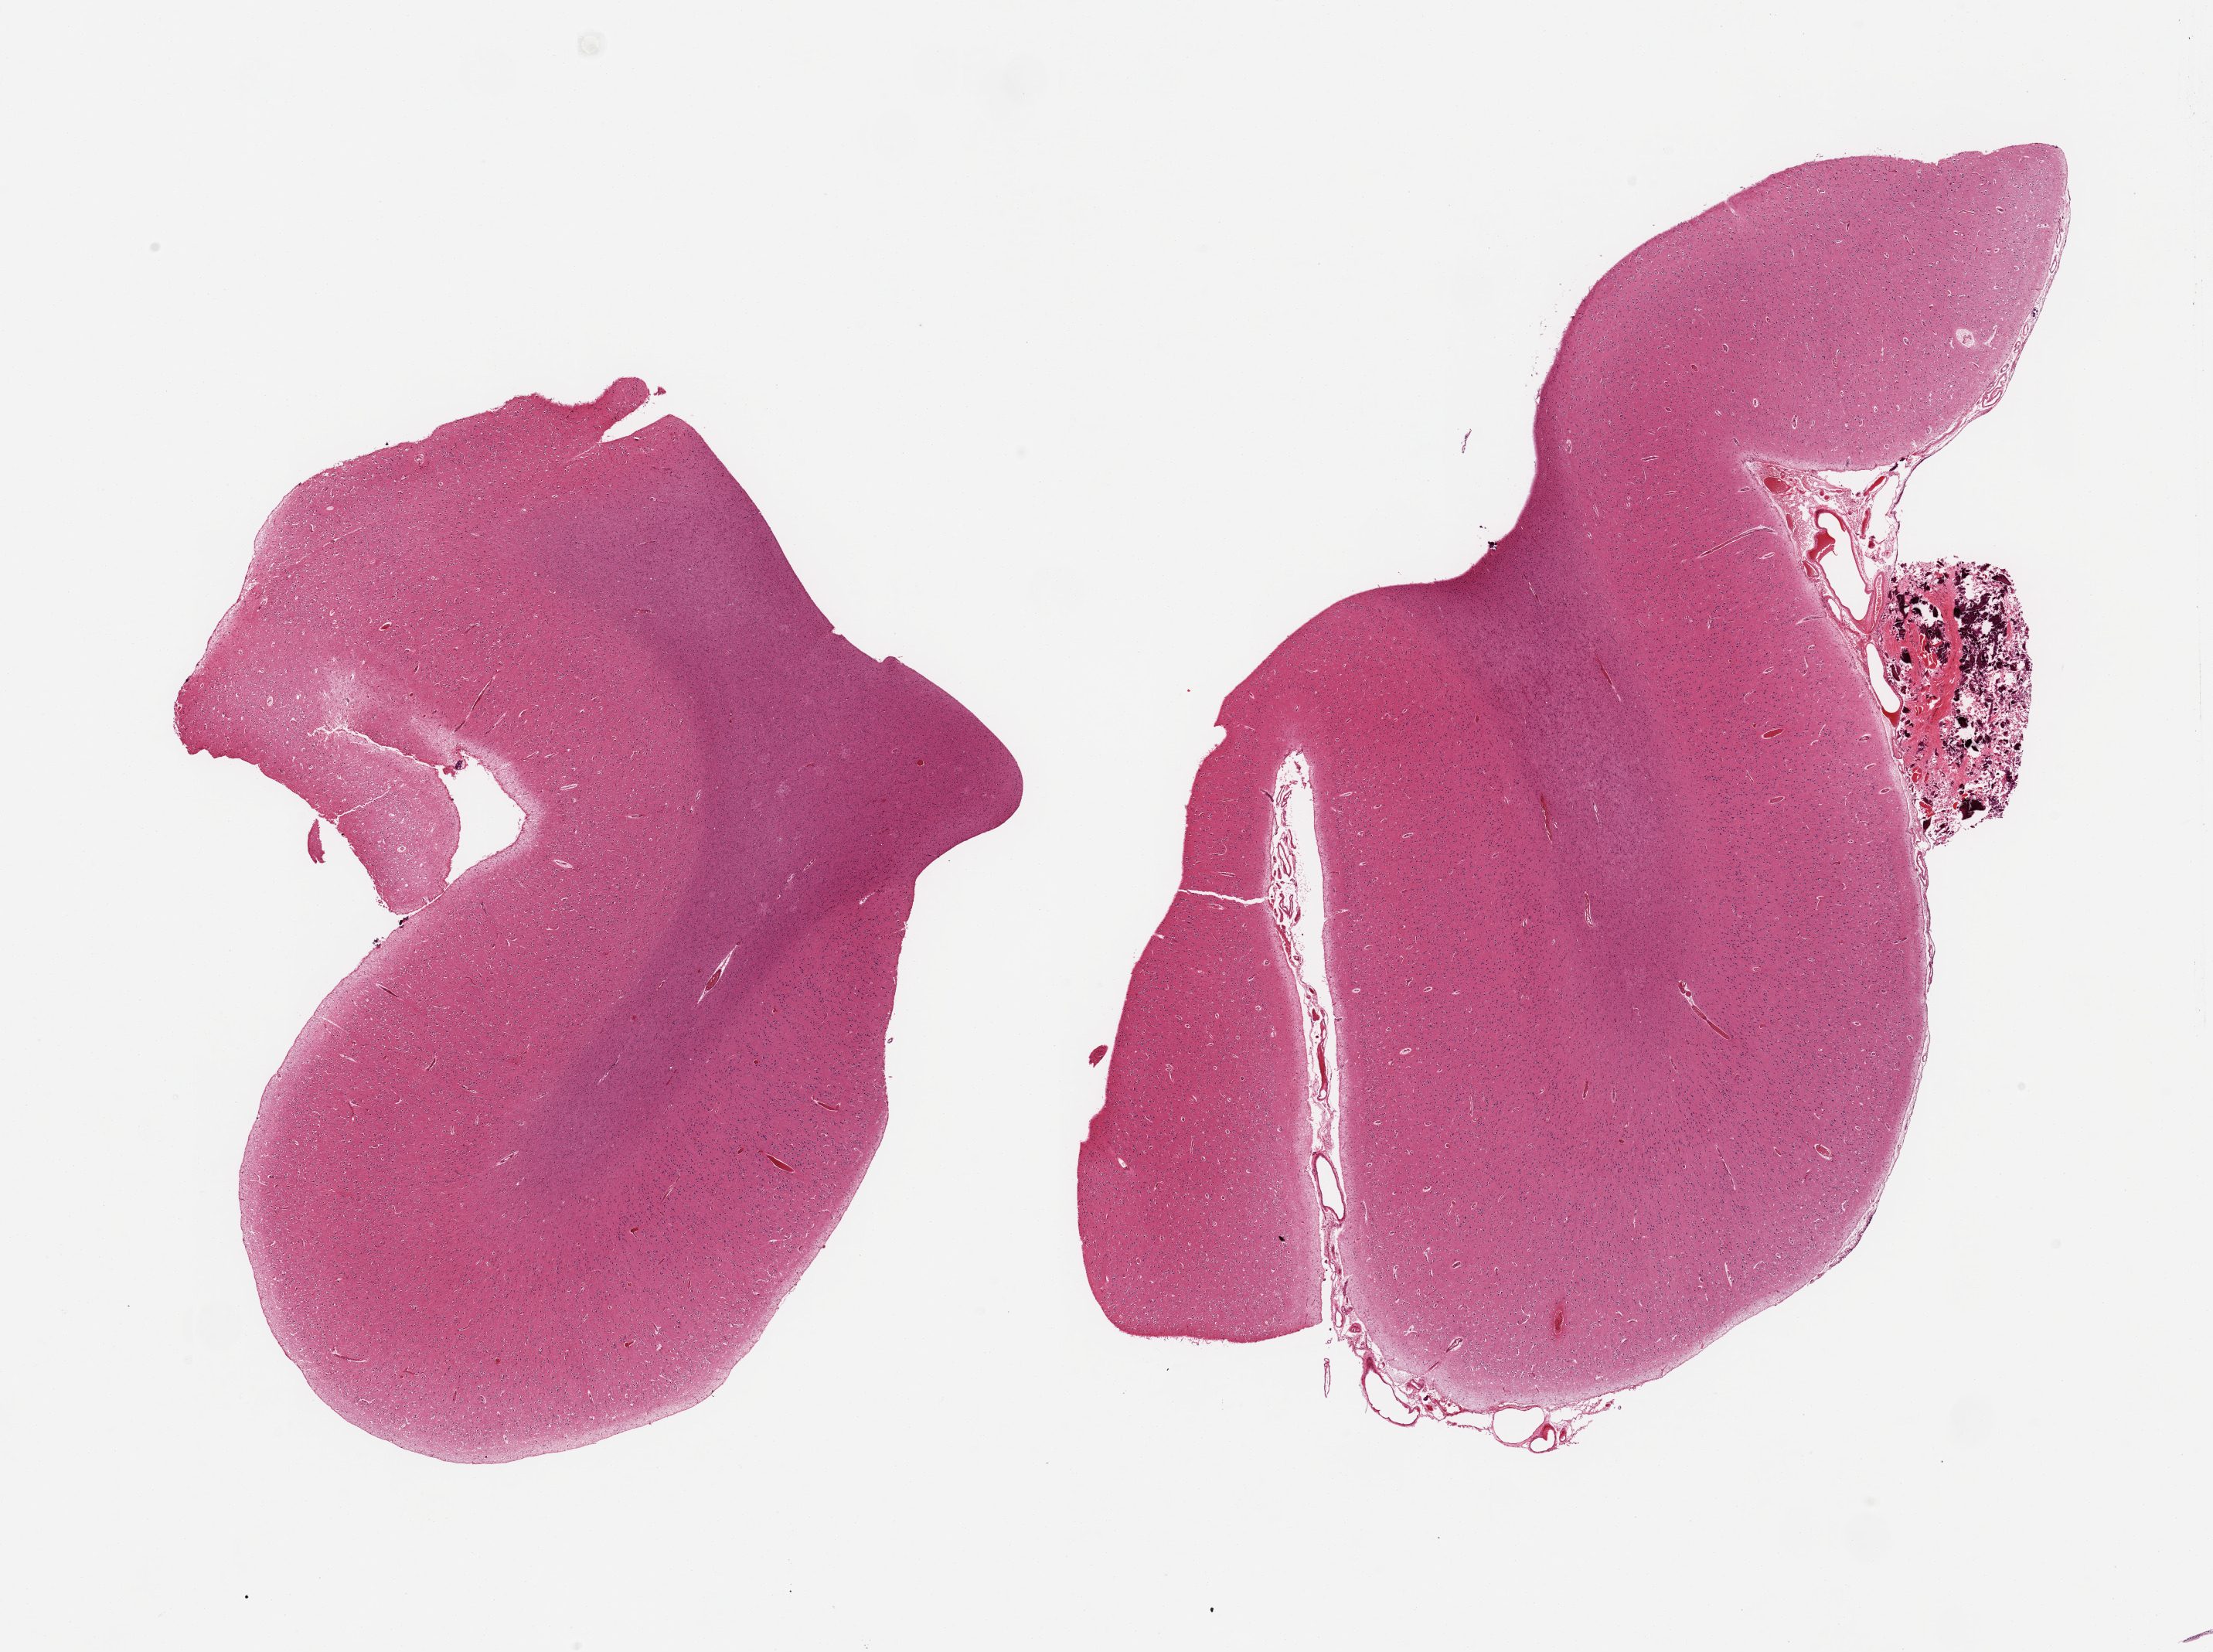
Digitized haematoxylin and eosin-stained section, brightfield — a low-resolution overview of the entire scanned area, about 22.6 x 16.9 mm, PAXgene-fixed, paraffin-embedded tissue, section of cerebral cortex (target tissue), tissue donor sample. Donor sex: male.
- review note (as recorded): 2 pieces, no abnormalities